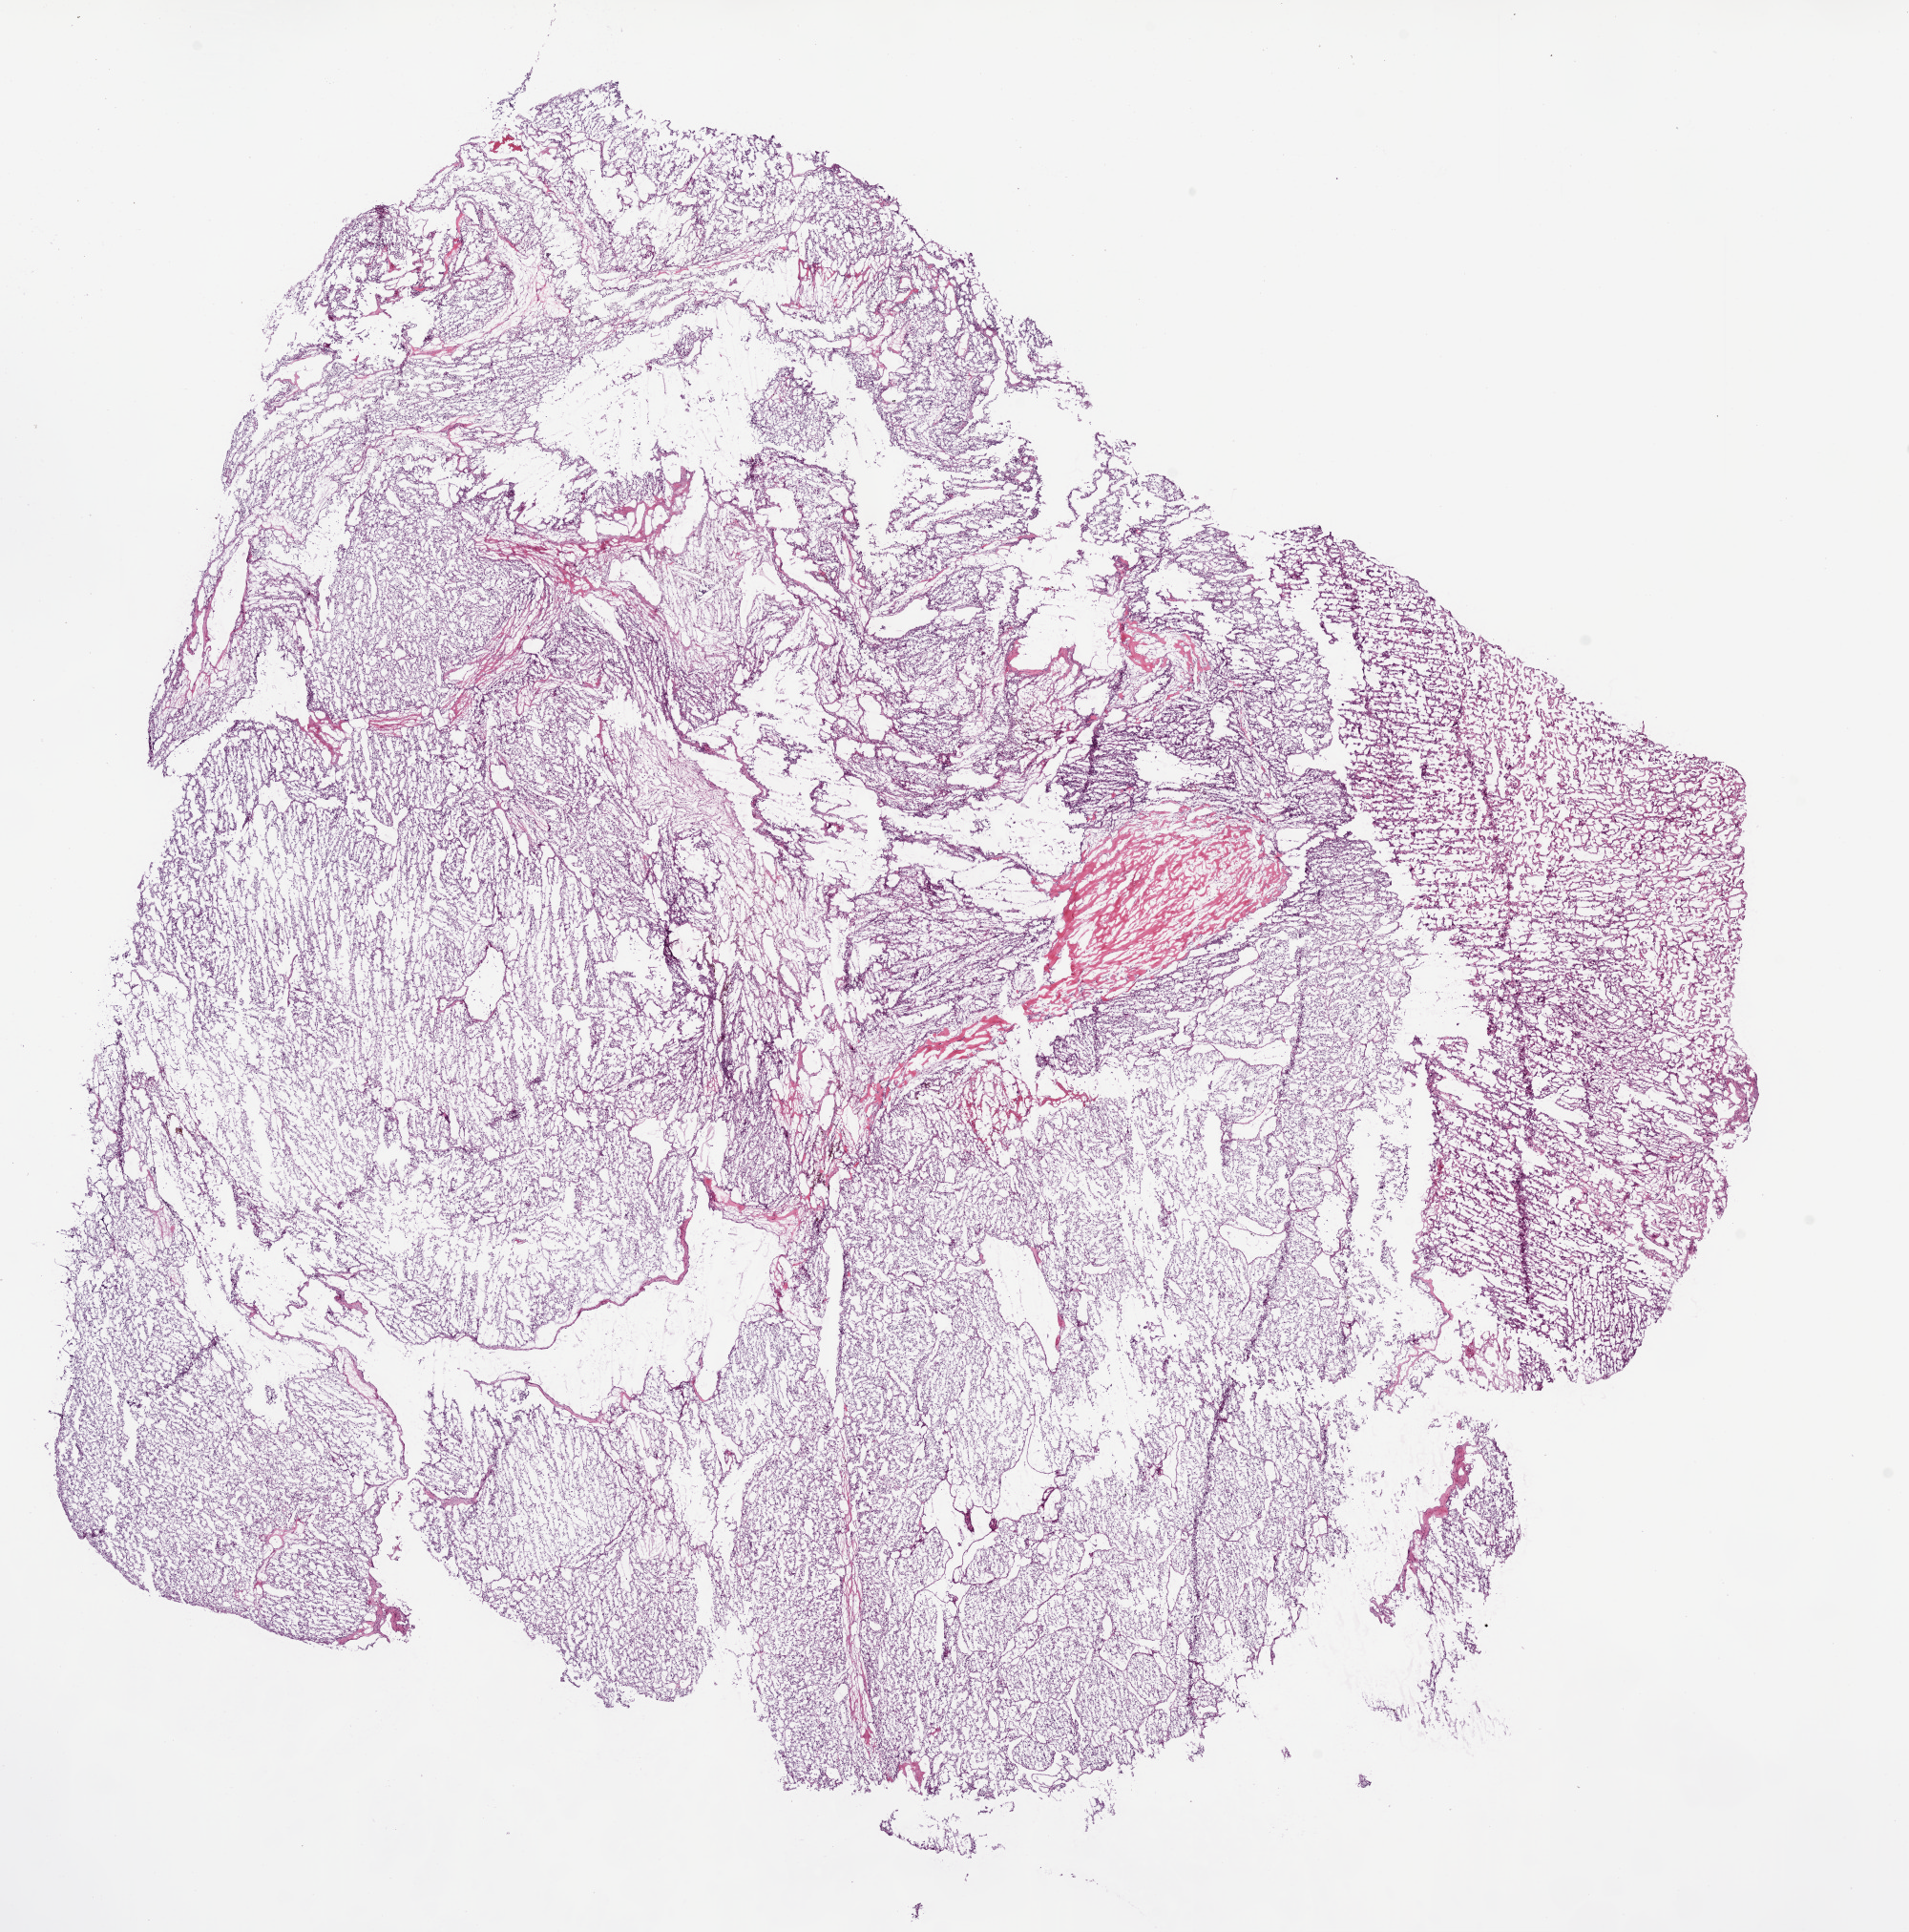
H&E-stained whole-slide image, low-resolution overview of the scanned area, about 16.0 x 16.2 mm, frozen section, kidney, primary tumour sample. Patient: male, age at initial diagnosis 58 years. Histologic grade: G4 (undifferentiated). Pathologist review of this section (percent, as recorded): tumour cells 90%, tumour nuclei 85%, normal cells 0%, stromal cells 10%, necrosis 0%.
Lymph nodes positive (case pathology): 0 of 4 examined. AJCC pathologic stage: II. Diagnosis: Clear cell adenocarcinoma, NOS.